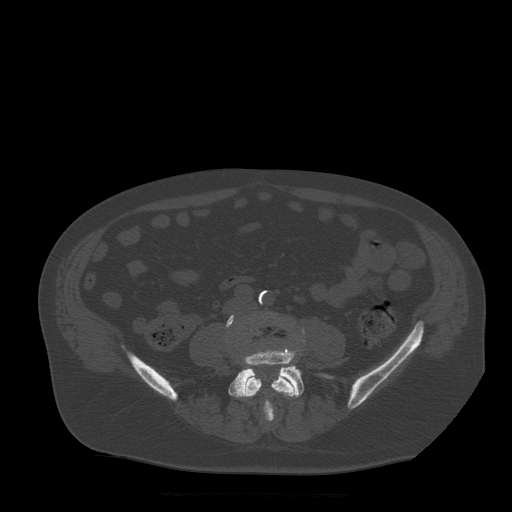
CT including the spine, one axial slice; position 101 of 522 along the scan axis; bone window (W 1800 / L 400 HU); 512 × 512 image matrix, field of view 420 × 420 mm. Patient age 72 years. Case-level facts recorded for this patient, not image findings: primary cancer: prostate.
Structures marked on this image (semi-automatic segmentation, software-assisted and operator-edited):
- L4 vertebra: bounding box [x1, y1, x2, y2] px = [228, 315, 298, 415]
- L5 vertebra: [226, 316, 304, 421]